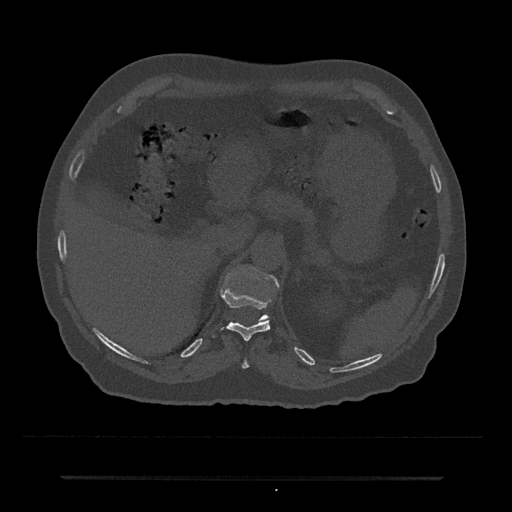
CT including the spine, one axial slice. Reconstruction kernel Br40s/3. 120 kVp. Bone window (W 1800 / L 400 HU). 0.5 mm slice thickness. 512 × 512 image matrix, field of view 437 × 437 mm. Male patient, age 69 years. Case-level facts recorded for this patient, not image findings: primary cancer: prostate.
Outlined on this slice (semi-automatic segmentation, software-assisted and operator-edited):
- T10 vertebra: bounding box (x1, y1, x2, y2) in pixels: (241, 358, 249, 369)
- T11 vertebra: (212, 289, 272, 341)
- T12 vertebra: (260, 275, 279, 320)